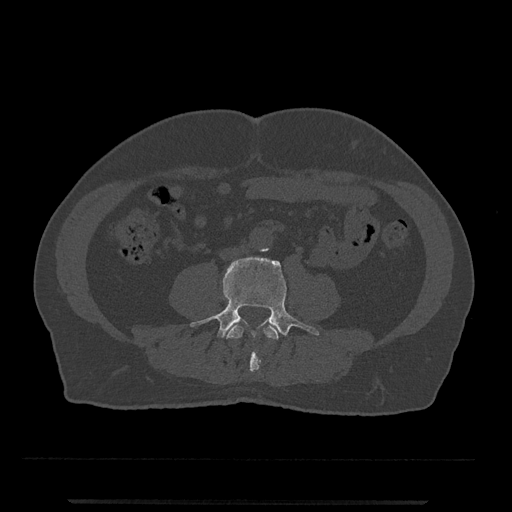
CT including the spine, one axial slice. Reconstruction kernel Br40s/3. Bone window (W 1800 / L 400 HU). 0.5 mm slice thickness. 512 × 512 image matrix, field of view 419 × 419 mm. Patient: male, 63 years. Case-level facts recorded for this patient, not image findings: primary cancer: prostate.
Annotated regions visible in this slice (semi-automatically segmented with operator editing):
- L3 vertebra: bounding box (x1, y1, x2, y2) in pixels: (226, 324, 281, 374)
- L4 vertebra: (190, 256, 319, 339)